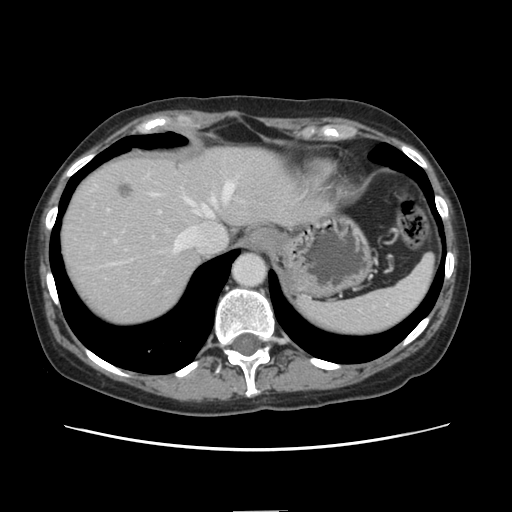
Contrast-enhanced abdominal CT, one axial slice; slice 117 of 141 in the series (ordered by position); 120 kVp; intravenous contrast given; soft-tissue window (W 400 / L 40 HU); 2.5 mm slice thickness; 512 × 512 image matrix, field of view 350 × 350 mm. Female patient, age 63 years. Case-level facts recorded for this patient, not image findings: diagnosis: colorectal cancer liver metastases, imaged before liver resection; multiple liver metastases: yes; largest metastasis: 3.2 cm.
Outlined on this slice (manually delineated by an expert):
- hepatic veins: bounding box [x1, y1, x2, y2] px = [161, 183, 233, 255]
- liver: [60, 146, 323, 327]
- planned liver remnant (the part of the liver to remain after resection): [200, 147, 326, 230]
- portal vein (with intrahepatic branches): [152, 181, 230, 211]